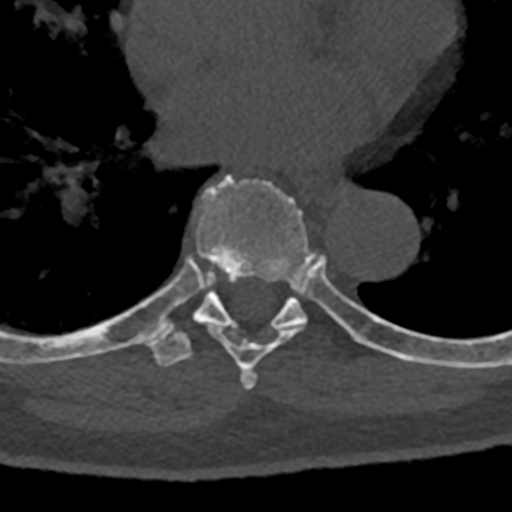
CT including the spine, one axial slice; position 739 of 797 along the scan axis; reconstruction kernel Br40s/3; 120 kVp; bone window (W 1800 / L 400 HU); 0.5 mm slice thickness; 512 × 512 image matrix. Patient: male, 74 years. From the clinical record (not read from this slice): primary cancer: renal.
Structures marked on this image (semi-automatically segmented with operator editing):
- T7 vertebra: bounding box [x1, y1, x2, y2] px = [171, 174, 372, 390]
- T8 vertebra: [70, 275, 432, 367]